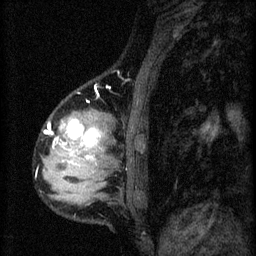
Breast MRI (dynamic contrast-enhanced), one sagittal slice. Position 14 of 60 along the scan axis. 3 images stored at this slice position (order not interpretable as contrast timing). 1.5 T. TE 4.2 ms, TR 8.2 ms. 2 mm slice thickness. 256 × 256 image matrix, field of view 180 × 180 mm. Patient: female, 37 years.
Outlined on this slice (semi-automatically segmented with operator editing):
- analysis volume of interest (the breast-tissue region the enhancement analysis was run in; not a lesion): bounding box [x1, y1, x2, y2] px = [44, 106, 119, 197]
- tumour enhancement mask (voxels above the 70 % enhancement threshold inside the analysis volume of interest): [49, 120, 101, 159]